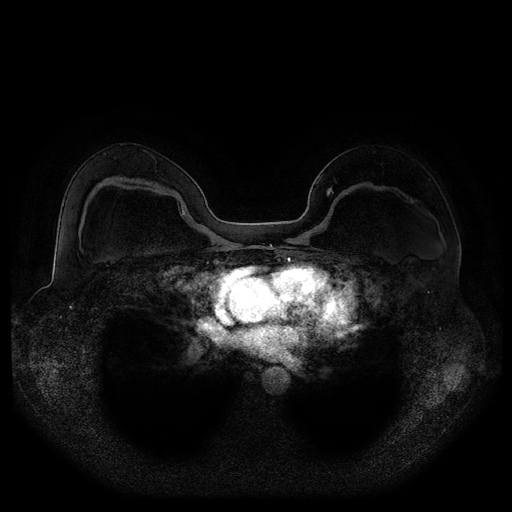
Breast MRI (dynamic contrast-enhanced, multi-phase), one axial slice; slice 65 of 116 in the series (ordered by position); dynamic contrast-enhanced series, time point 2 of 5 at this slice position (early post-contrast); 1.5 T; TE 2.5 ms, TR 5.2 ms; 2.1 mm slice thickness; 512 × 512 image matrix, field of view 380 × 380 mm. Female patient, age 43 years.
Structures marked on this image (semi-automatically segmented with operator editing):
- breast lesion (labelled benign in the annotation): box from (x=326, y=186) to (x=334, y=197) px